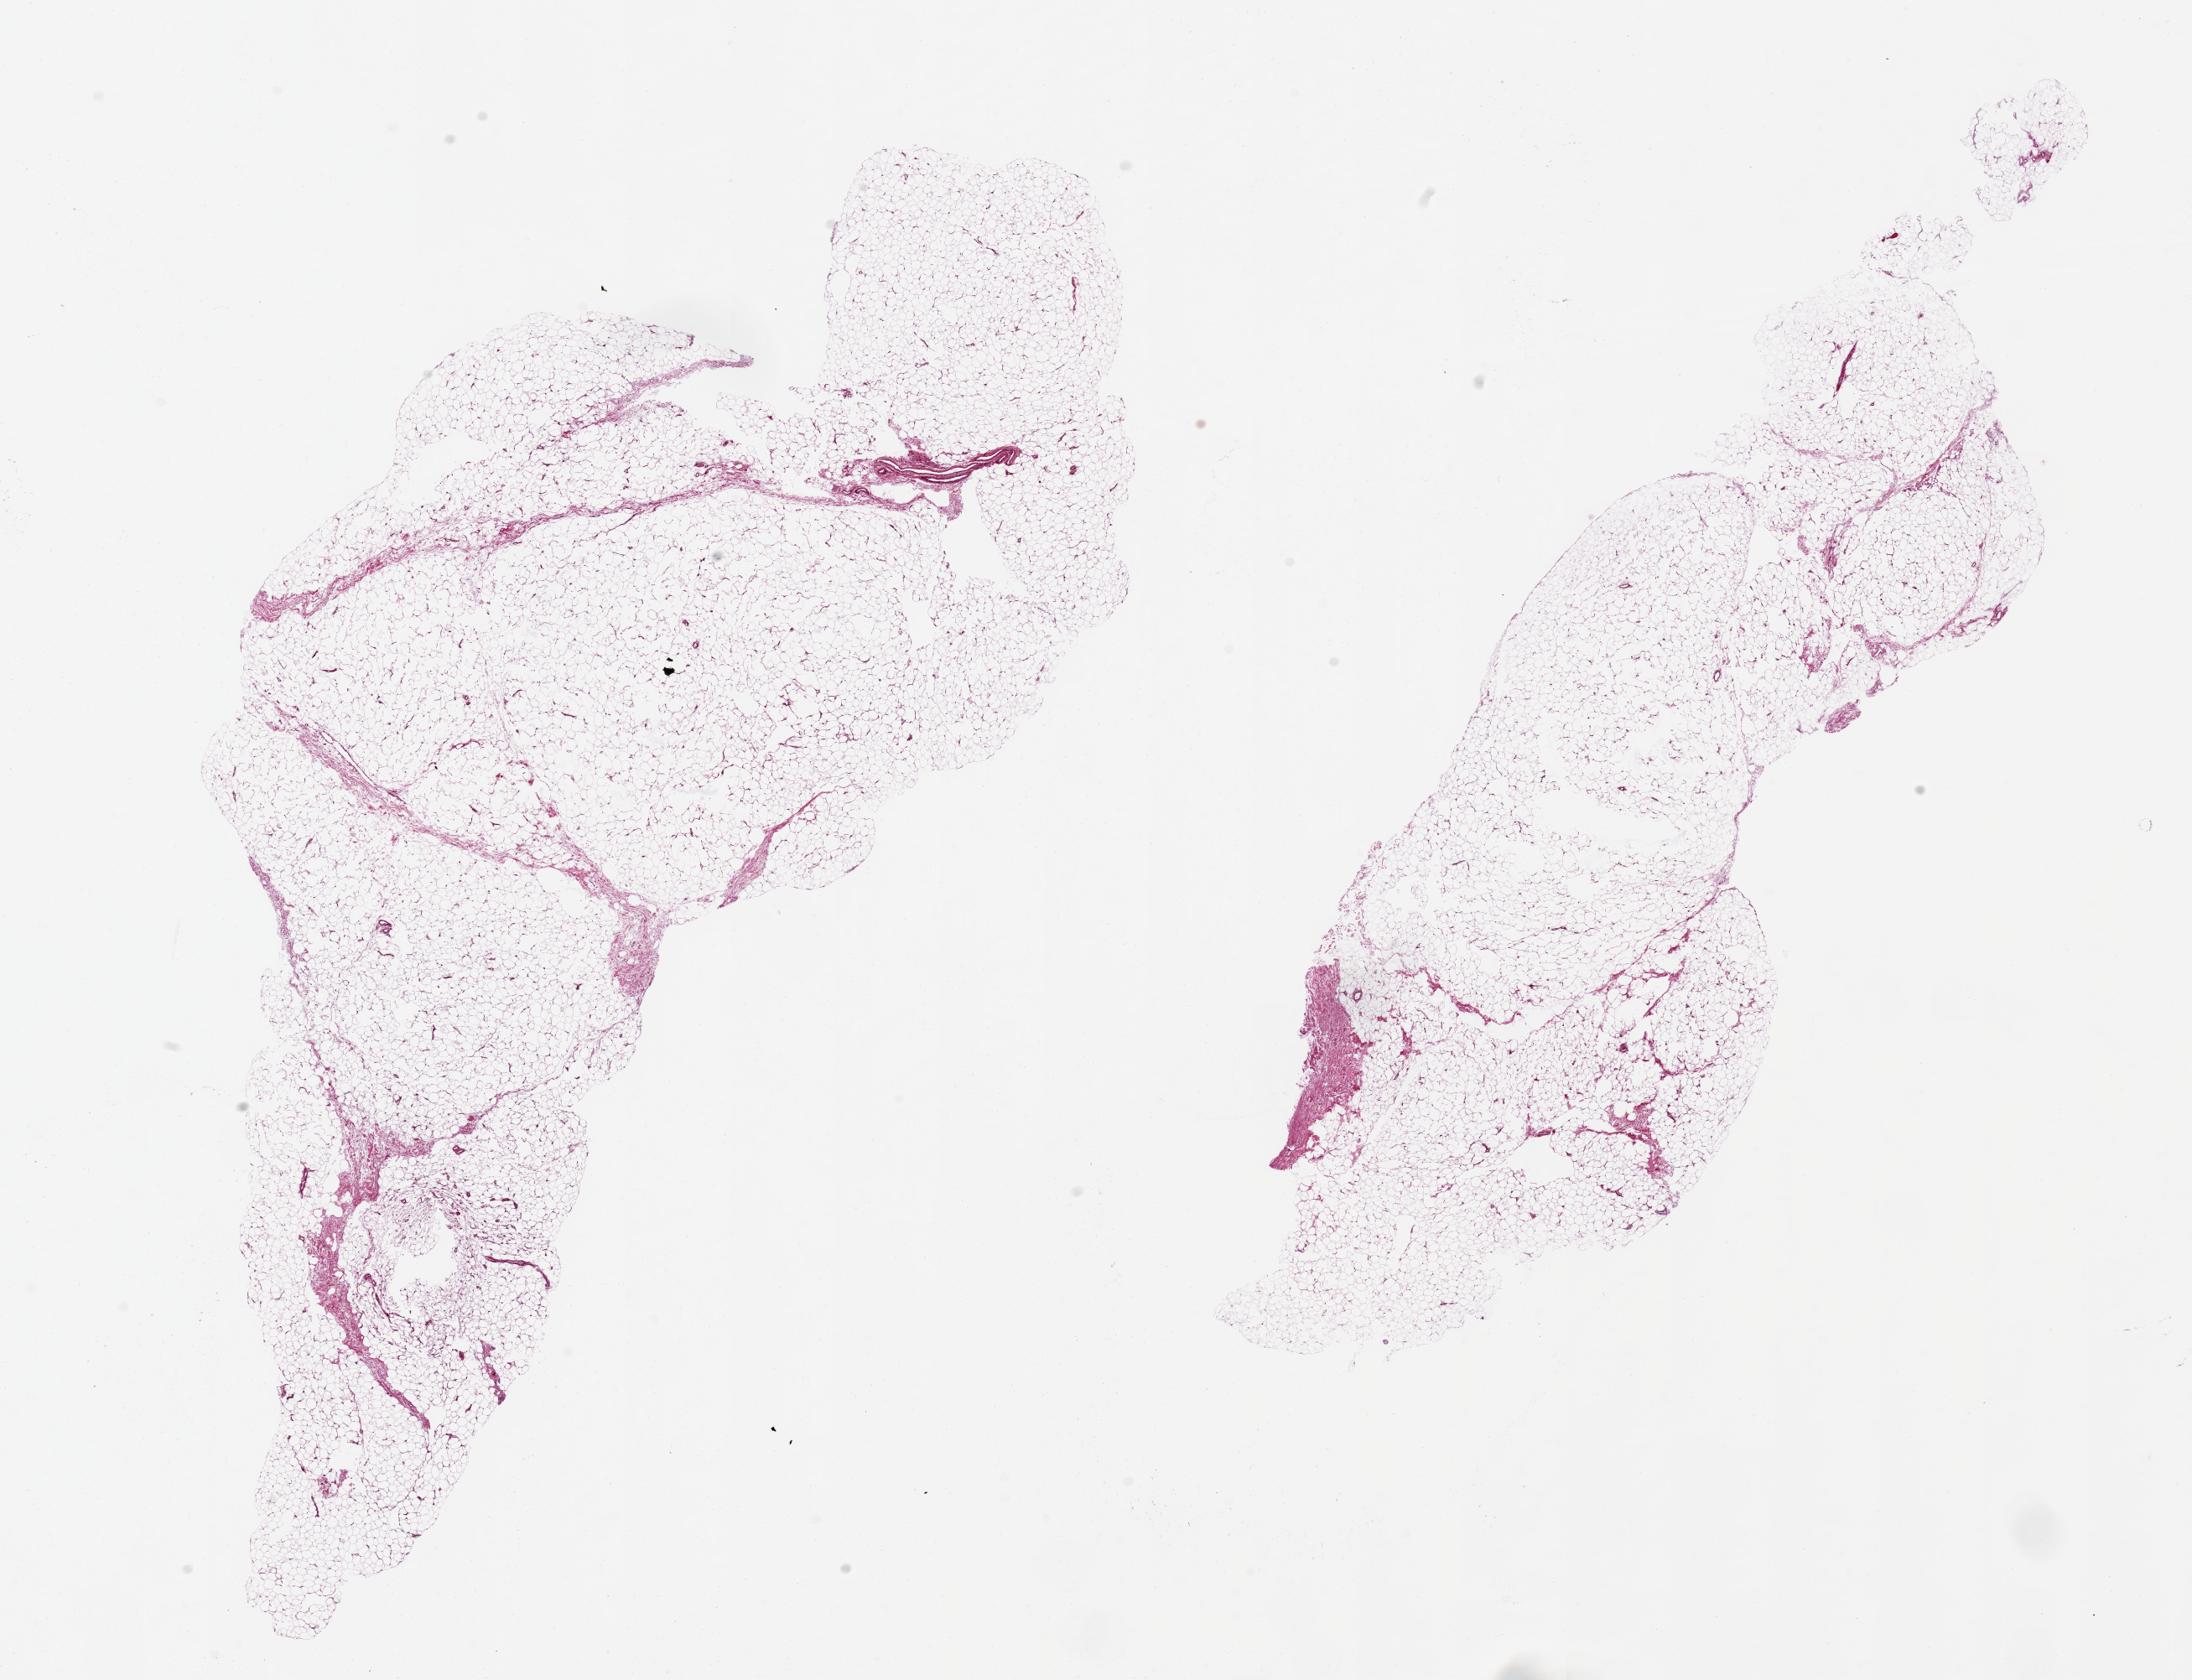
Digitized H&E-stained section, brightfield — shown as a low-resolution overview of the whole scanned area (about 20.7 x 15.8 mm, slide scanned at 20x), PAXgene-fixed, paraffin-embedded tissue, sampled site (target tissue): adipose tissue, donor tissue sample. Donor: female.
- review note (as recorded): 2 pieces 15x5 & 14x4mm; minimal artifacts